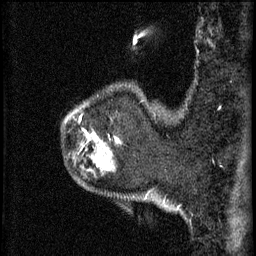
Breast MRI (dynamic contrast-enhanced), one sagittal slice; position 53 of 60 along the scan axis; 3 images stored at this slice position (order not interpretable as contrast timing); 1.5 T; TE 4.2 ms, TR 11 ms; 256 × 256 image matrix, field of view 180 × 180 mm. Female patient, age 52 years.
Annotated regions visible in this slice (semi-automatic segmentation, software-assisted and operator-edited):
- analysis volume of interest (the breast-tissue region the enhancement analysis was run in; not a lesion): bounding box [x1, y1, x2, y2] px = [86, 120, 124, 157]
- tumour enhancement mask (voxels above the 70 % enhancement threshold inside the analysis volume of interest): [86, 132, 88, 137]